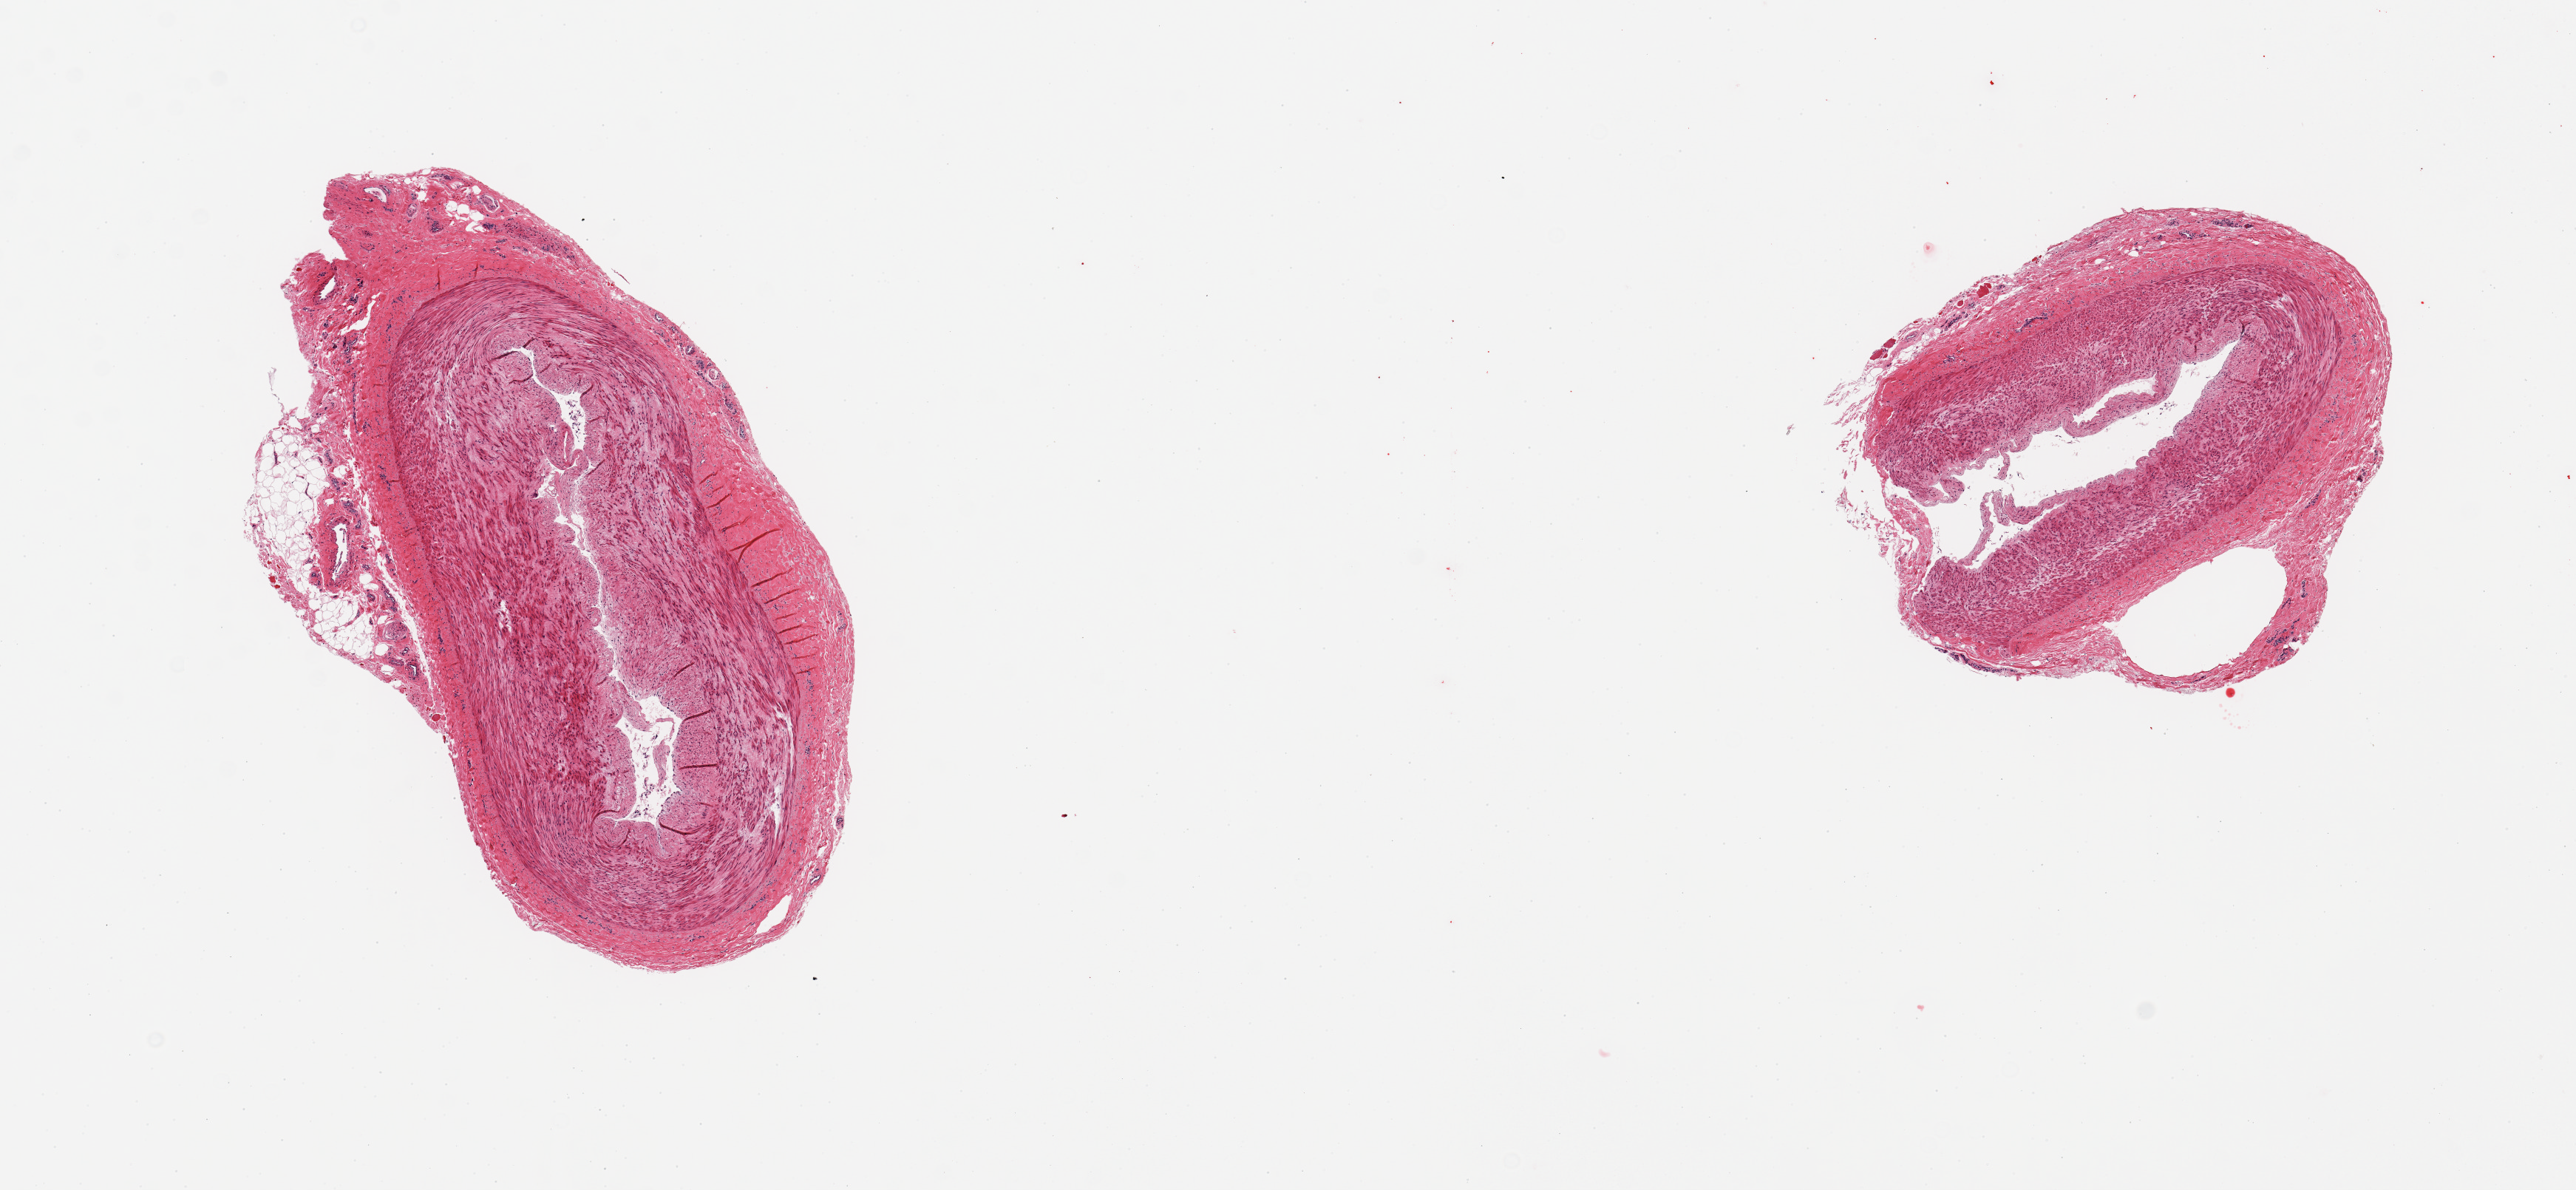
Haematoxylin and eosin whole-slide image, low-resolution overview of the scanned area, about 13.8 x 6.4 mm (slide scanned at 20x); PAXgene-fixed paraffin-embedded (PFPE) section; target tissue: tibial artery; tissue donor sample. Donor: male.
* pathologist's review note for this sample: 2 pieces; small attachment of fat on 1 piece